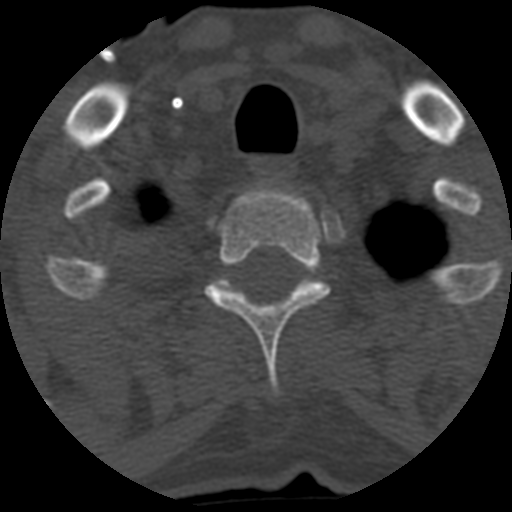
CT including the spine, one axial slice. Slice 503 of 708 in the series (ordered by position). One of 3 acquisitions stored at this slice position. Bone window (W 1800 / L 400 HU). 1.25 mm slice thickness. 512 × 512 image matrix, field of view 160 × 160 mm. Patient age 55 years. From the clinical record (not read from this slice): primary cancer: colon; vertebrae with lytic lesions (as recorded): T12, L1, L5.
Outlined on this slice (semi-automatic segmentation, software-assisted and operator-edited):
- T2 vertebra: bounding box (x1, y1, x2, y2) in pixels: (205, 184, 329, 396)
- T3 vertebra: (300, 283, 302, 285)